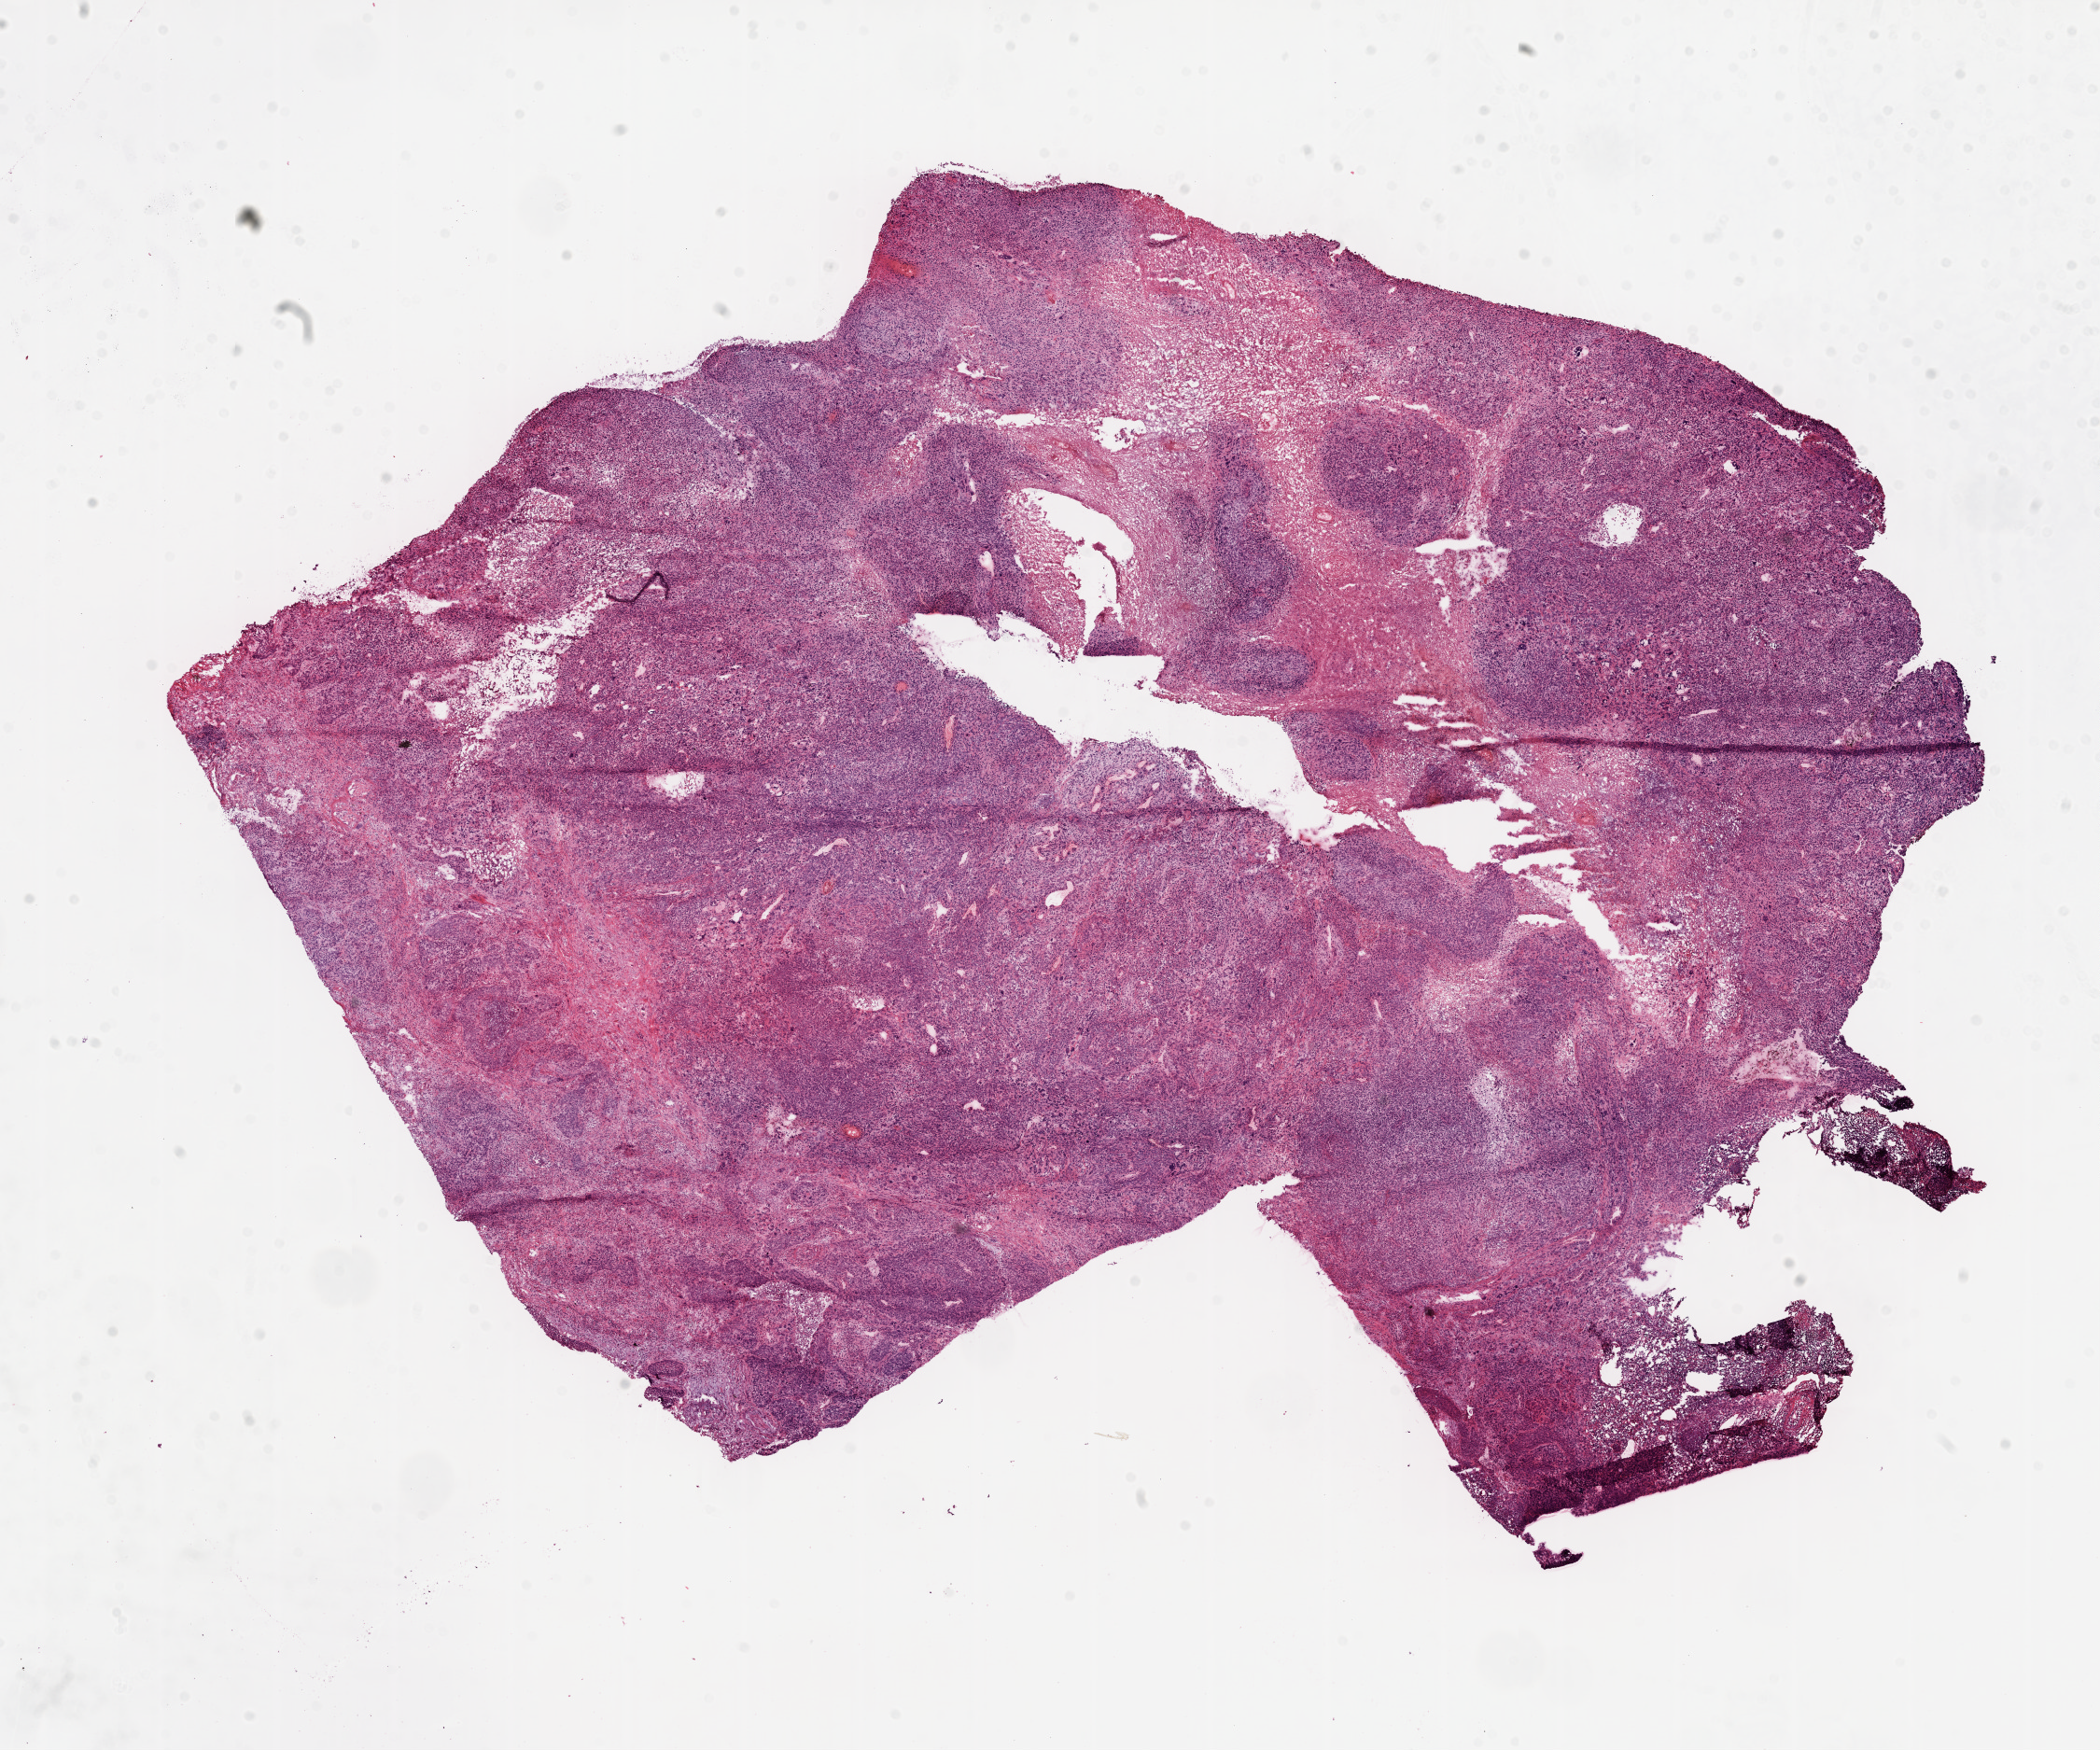
Whole-slide histology image, H&E — a low-resolution overview of the entire scanned area, about 18.1 x 15.0 mm. Frozen section from the top of the tissue portion. Lung, primary tumour sample. Patient: female, age at initial diagnosis 76 years. Pathologist review of this section (percent, as recorded): tumour cells 60%, tumour nuclei 70%, normal cells 0%, stromal cells 20%, necrosis 20%.
Histologic diagnosis: Squamous cell carcinoma, NOS. TNM: T2 N0 M0. AJCC pathologic stage: IB (5th edition).